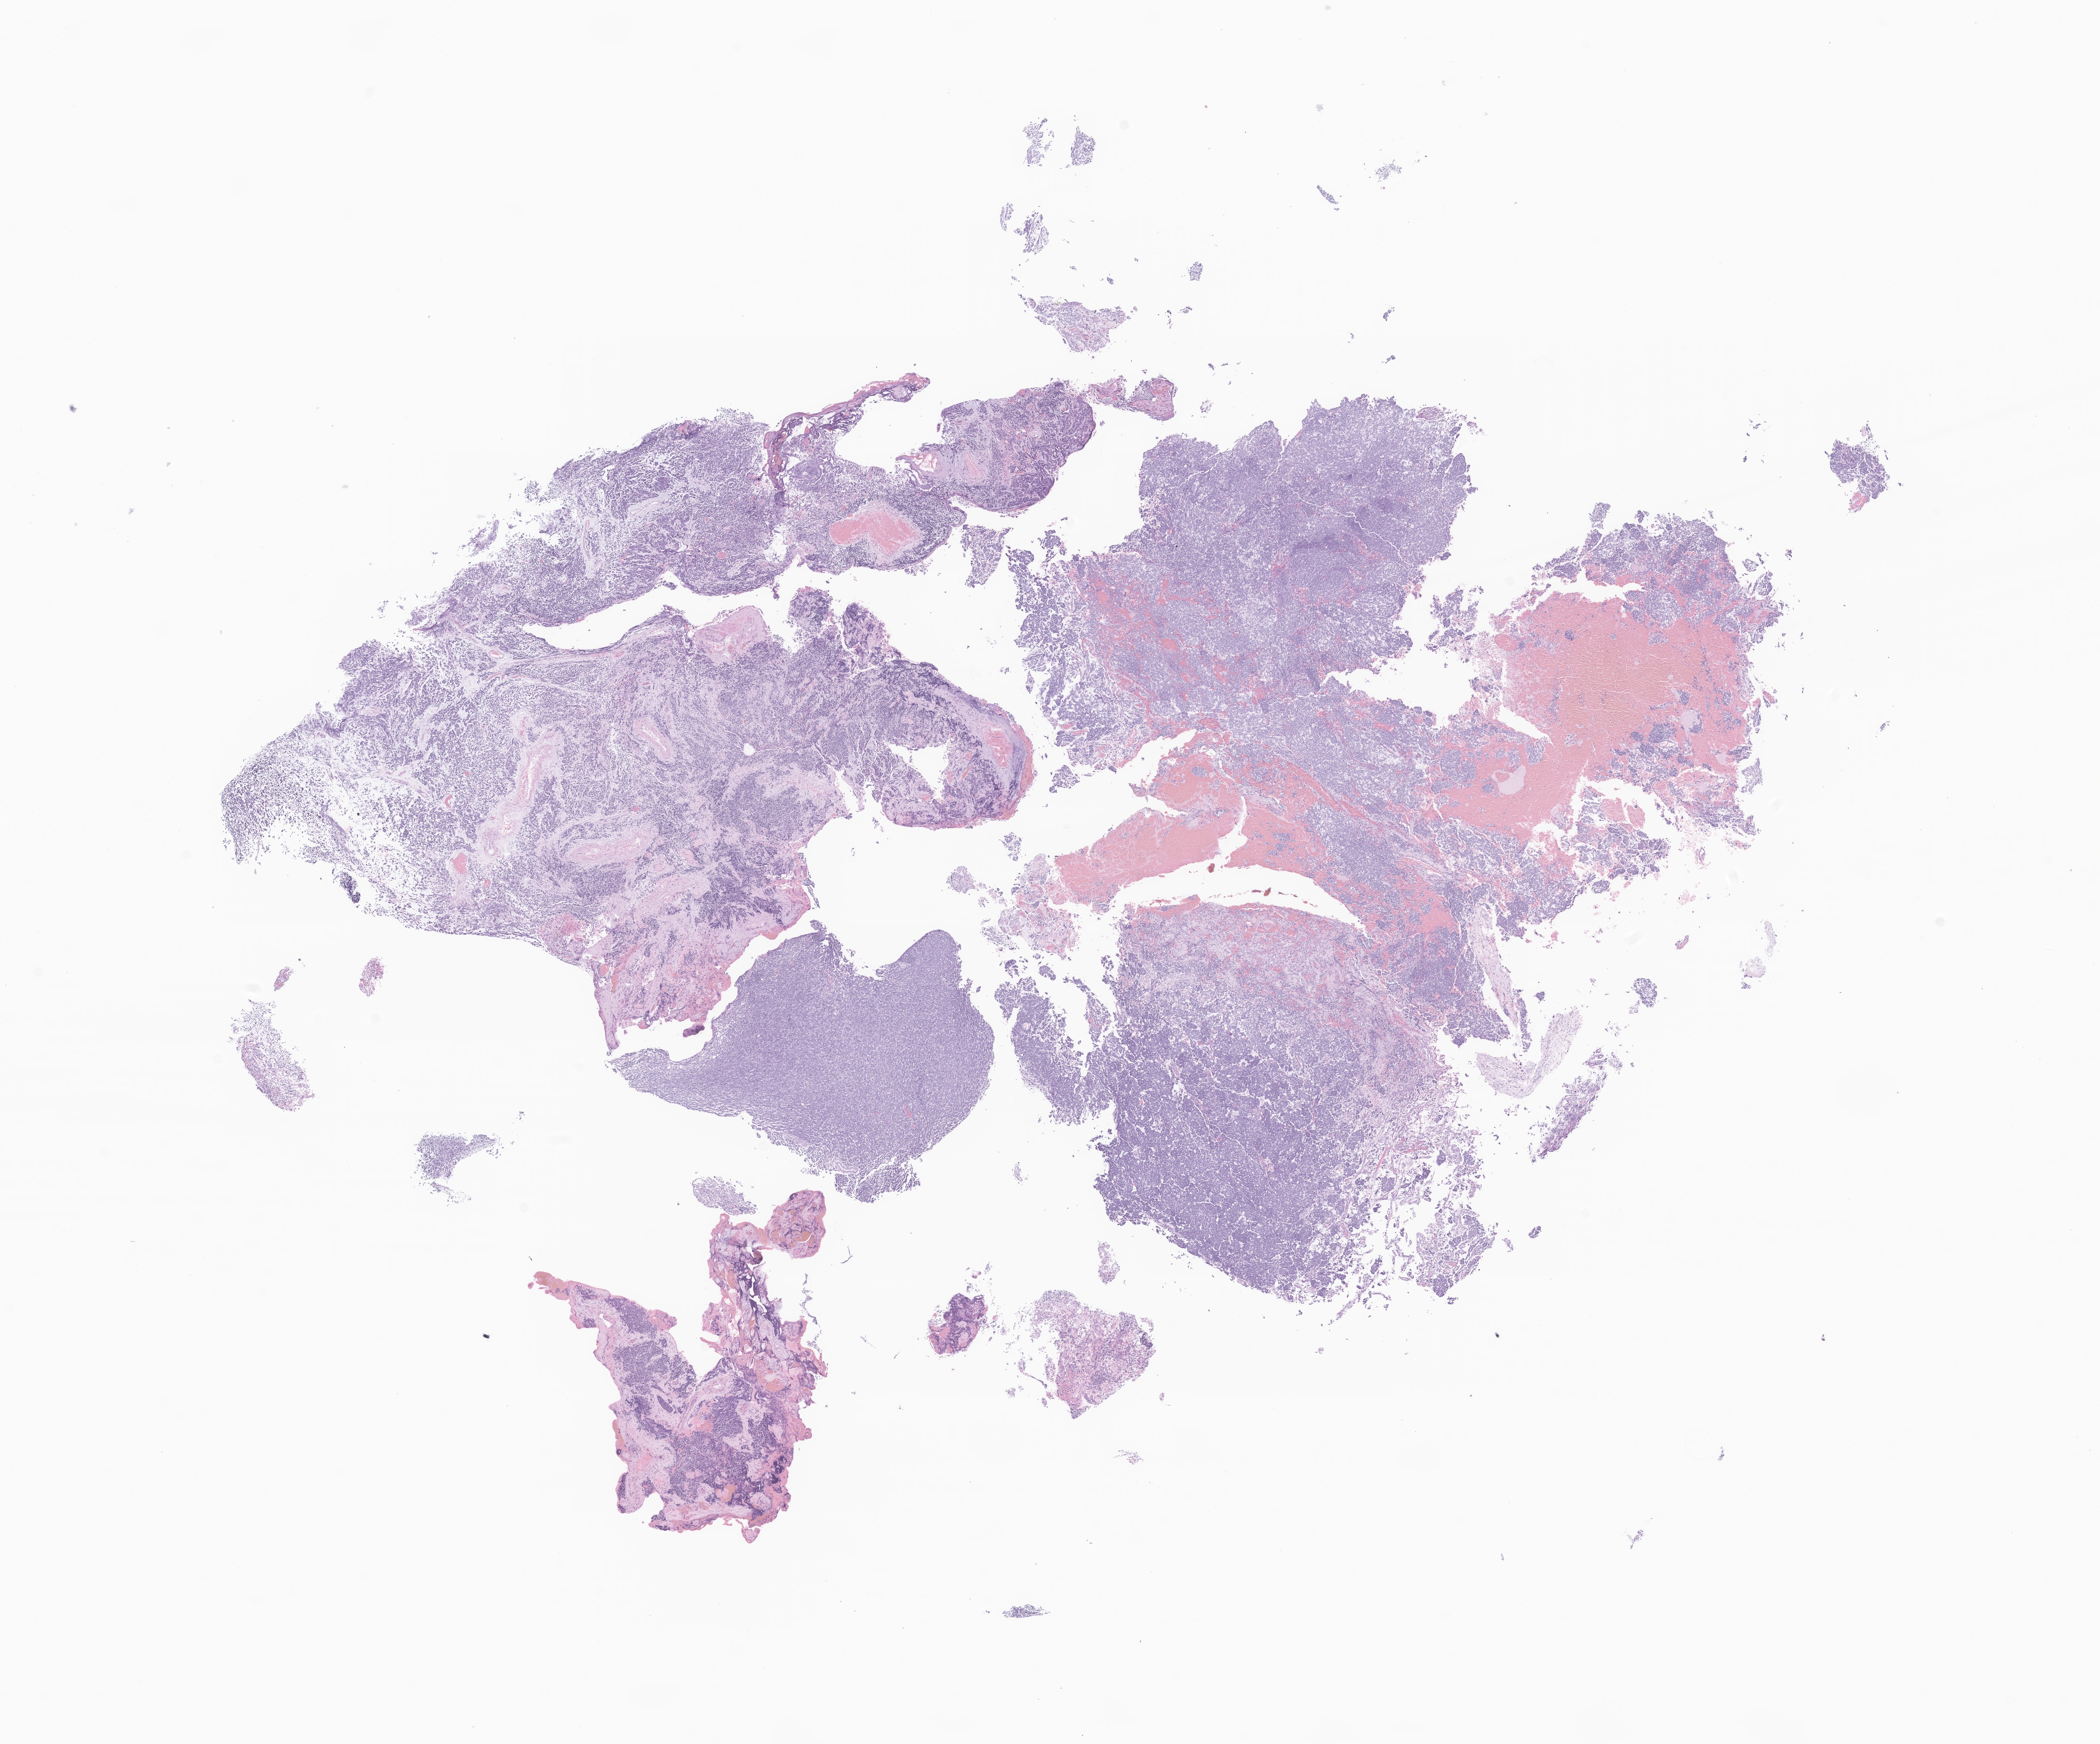
Haematoxylin and eosin whole-slide image of tumor tissue from the cerebellum, shown as a low-resolution overview of the whole scanned area (about 19.0 x 15.8 mm). Formalin-fixed paraffin-embedded section. Male patient, age 903 days (about 2.5 years).
• diagnosis (ICD-O-3 morphology term): Medulloblastoma, NOS